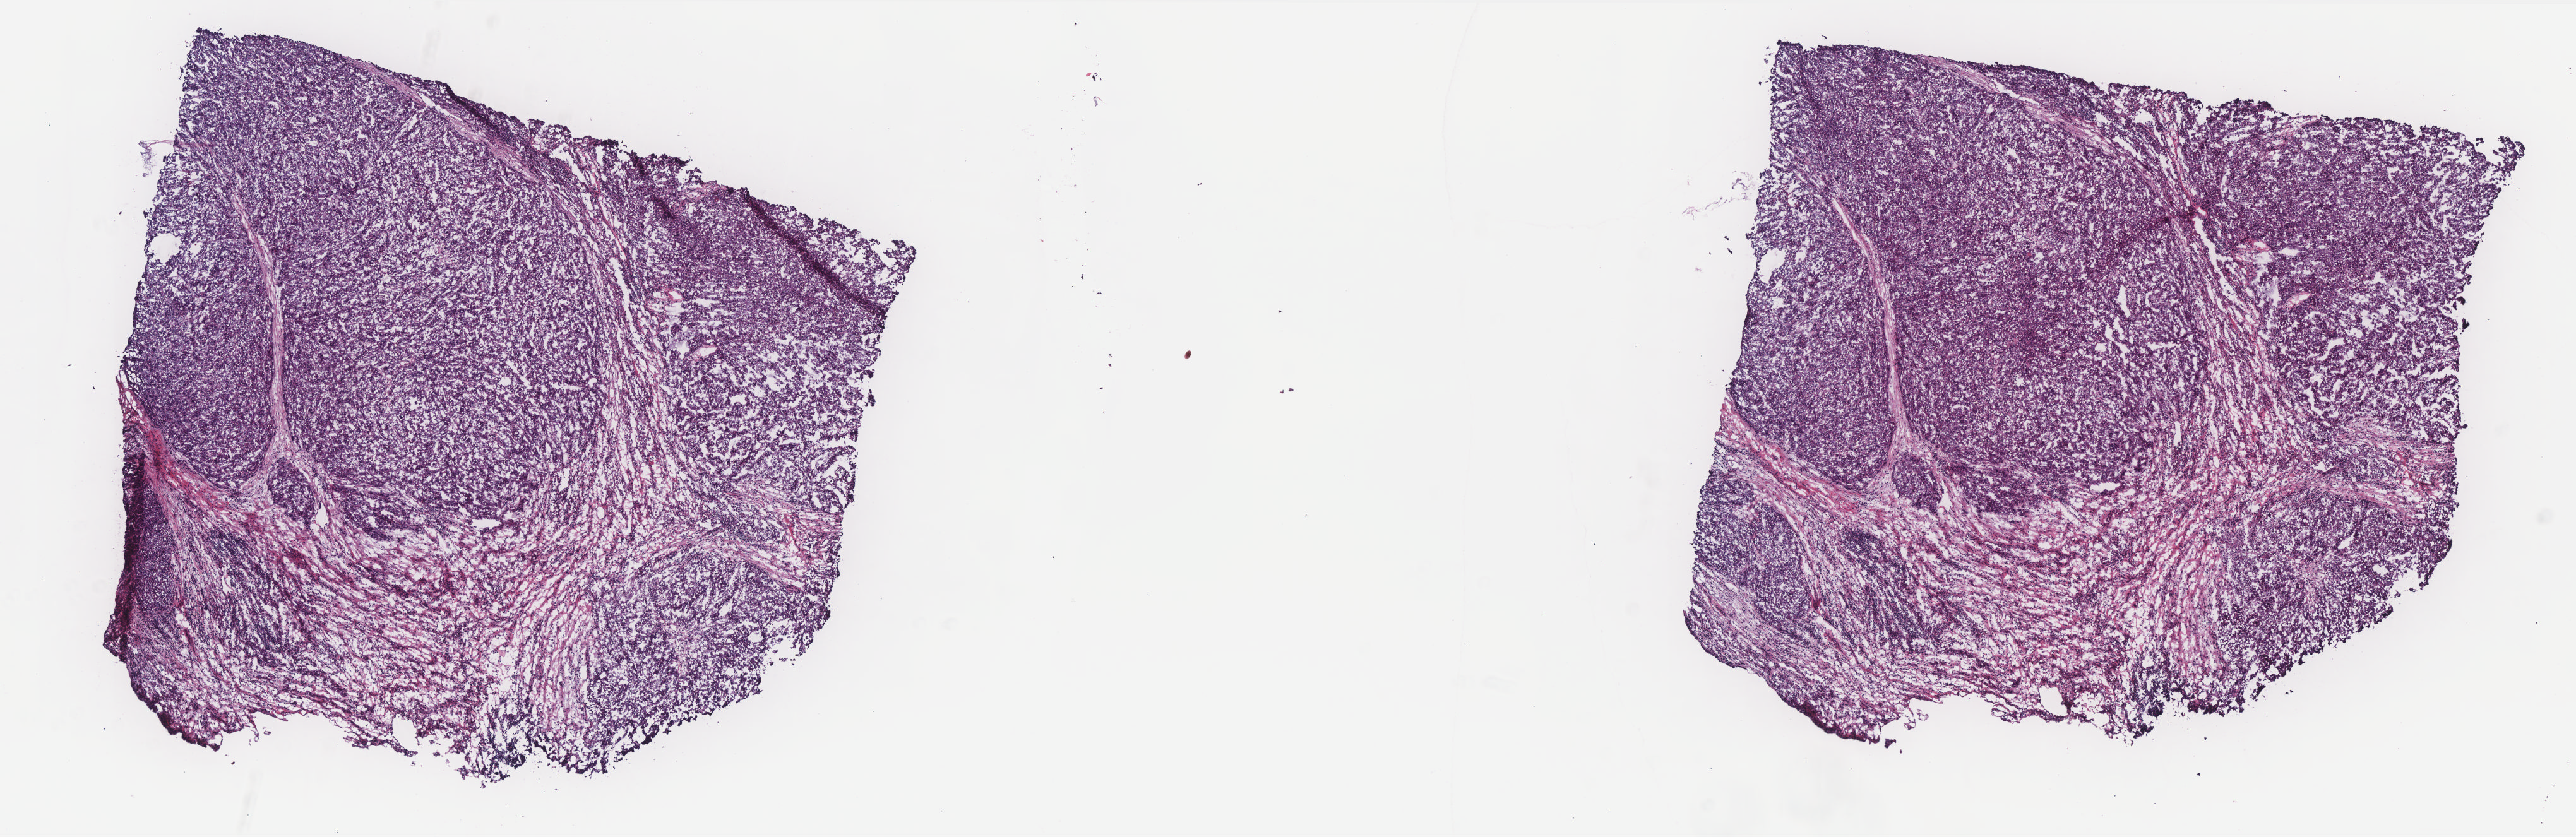
Whole-slide histology image, H&E-stained, low-resolution overview of the scanned area, about 16.4 x 5.3 mm; frozen section from the top of the tissue portion; primary tumour sample from the liver. Female, age 57 years at initial diagnosis. Slide review estimates, as recorded: tumour cells 85%, tumour nuclei 80%.
Pathologic diagnosis: Hepatocellular carcinoma, NOS.